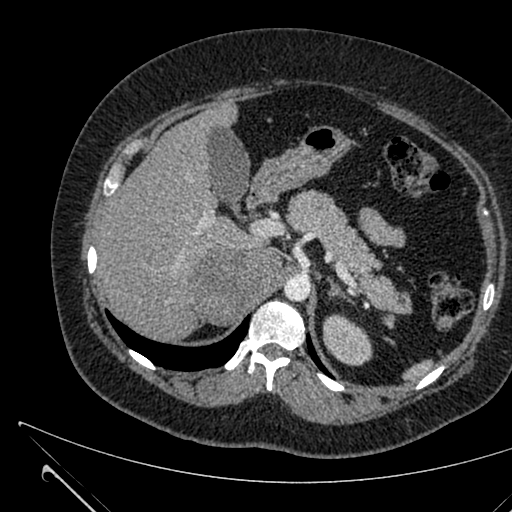
Contrast-enhanced abdominal CT, one axial slice. 120 kVp. Soft-tissue window (W 400 / L 40 HU). 512 × 512 image matrix, field of view 376 × 376 mm. Female patient, age 36 years. From the clinical record (not read from this slice): diagnosis: adrenocortical carcinoma; tumour side: right adrenal; tumour size at pathology: 10 cm; Ki-67 index: 20 %; stage (as recorded): 4.
Structures marked on this image (semi-automatically segmented with operator editing):
- mass: bounding box [x1, y1, x2, y2] px = [194, 249, 280, 323]